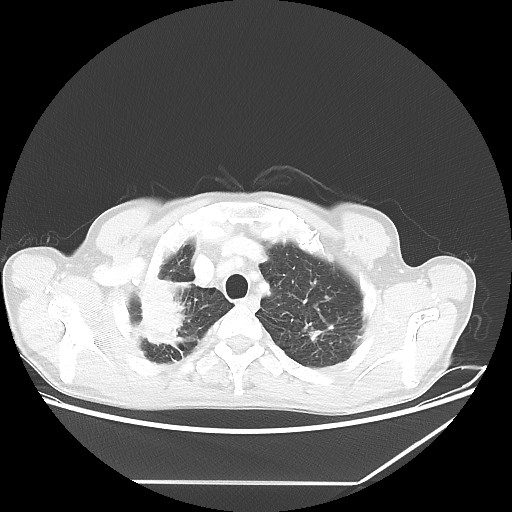
Chest CT, one axial slice. Slice 55 of 65 in the series (ordered by position). Lung window (W 1500 / L -600 HU). 5 mm slice thickness. 512 × 512 image matrix, field of view 397 × 397 mm. Male patient, age 68 years. From the clinical record (not read from this slice): clinical TNM (as recorded): T3 N3 M0.
Outlined on this slice (bounding box drawn by a radiologist):
- lung tumour (recorded histology: adenocarcinoma): bounding box [x1, y1, x2, y2] px = [122, 273, 192, 353]